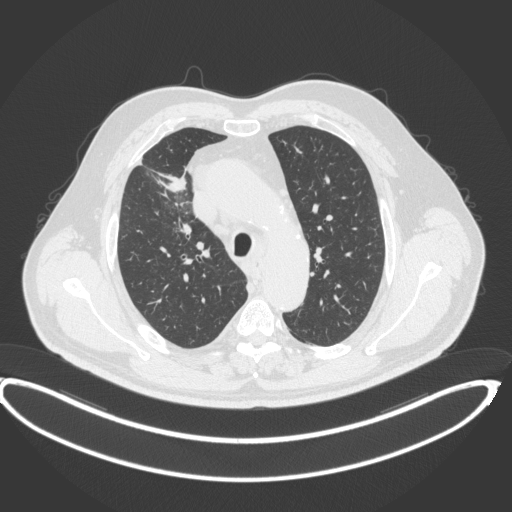
Chest CT, one axial slice. Slice 302 of 395 in the series (ordered by position). Lung window (W 1500 / L -600 HU). 1 mm slice thickness. 512 × 512 image matrix, field of view 448 × 448 mm. Patient: male, 62 years. From the clinical record (not read from this slice): clinical TNM (as recorded): T1c N3 M1c.
Outlined on this slice (rectangle marked by the reading radiologist):
- lung tumour (recorded histology: adenocarcinoma): bounding box [x1, y1, x2, y2] px = [161, 173, 187, 196]